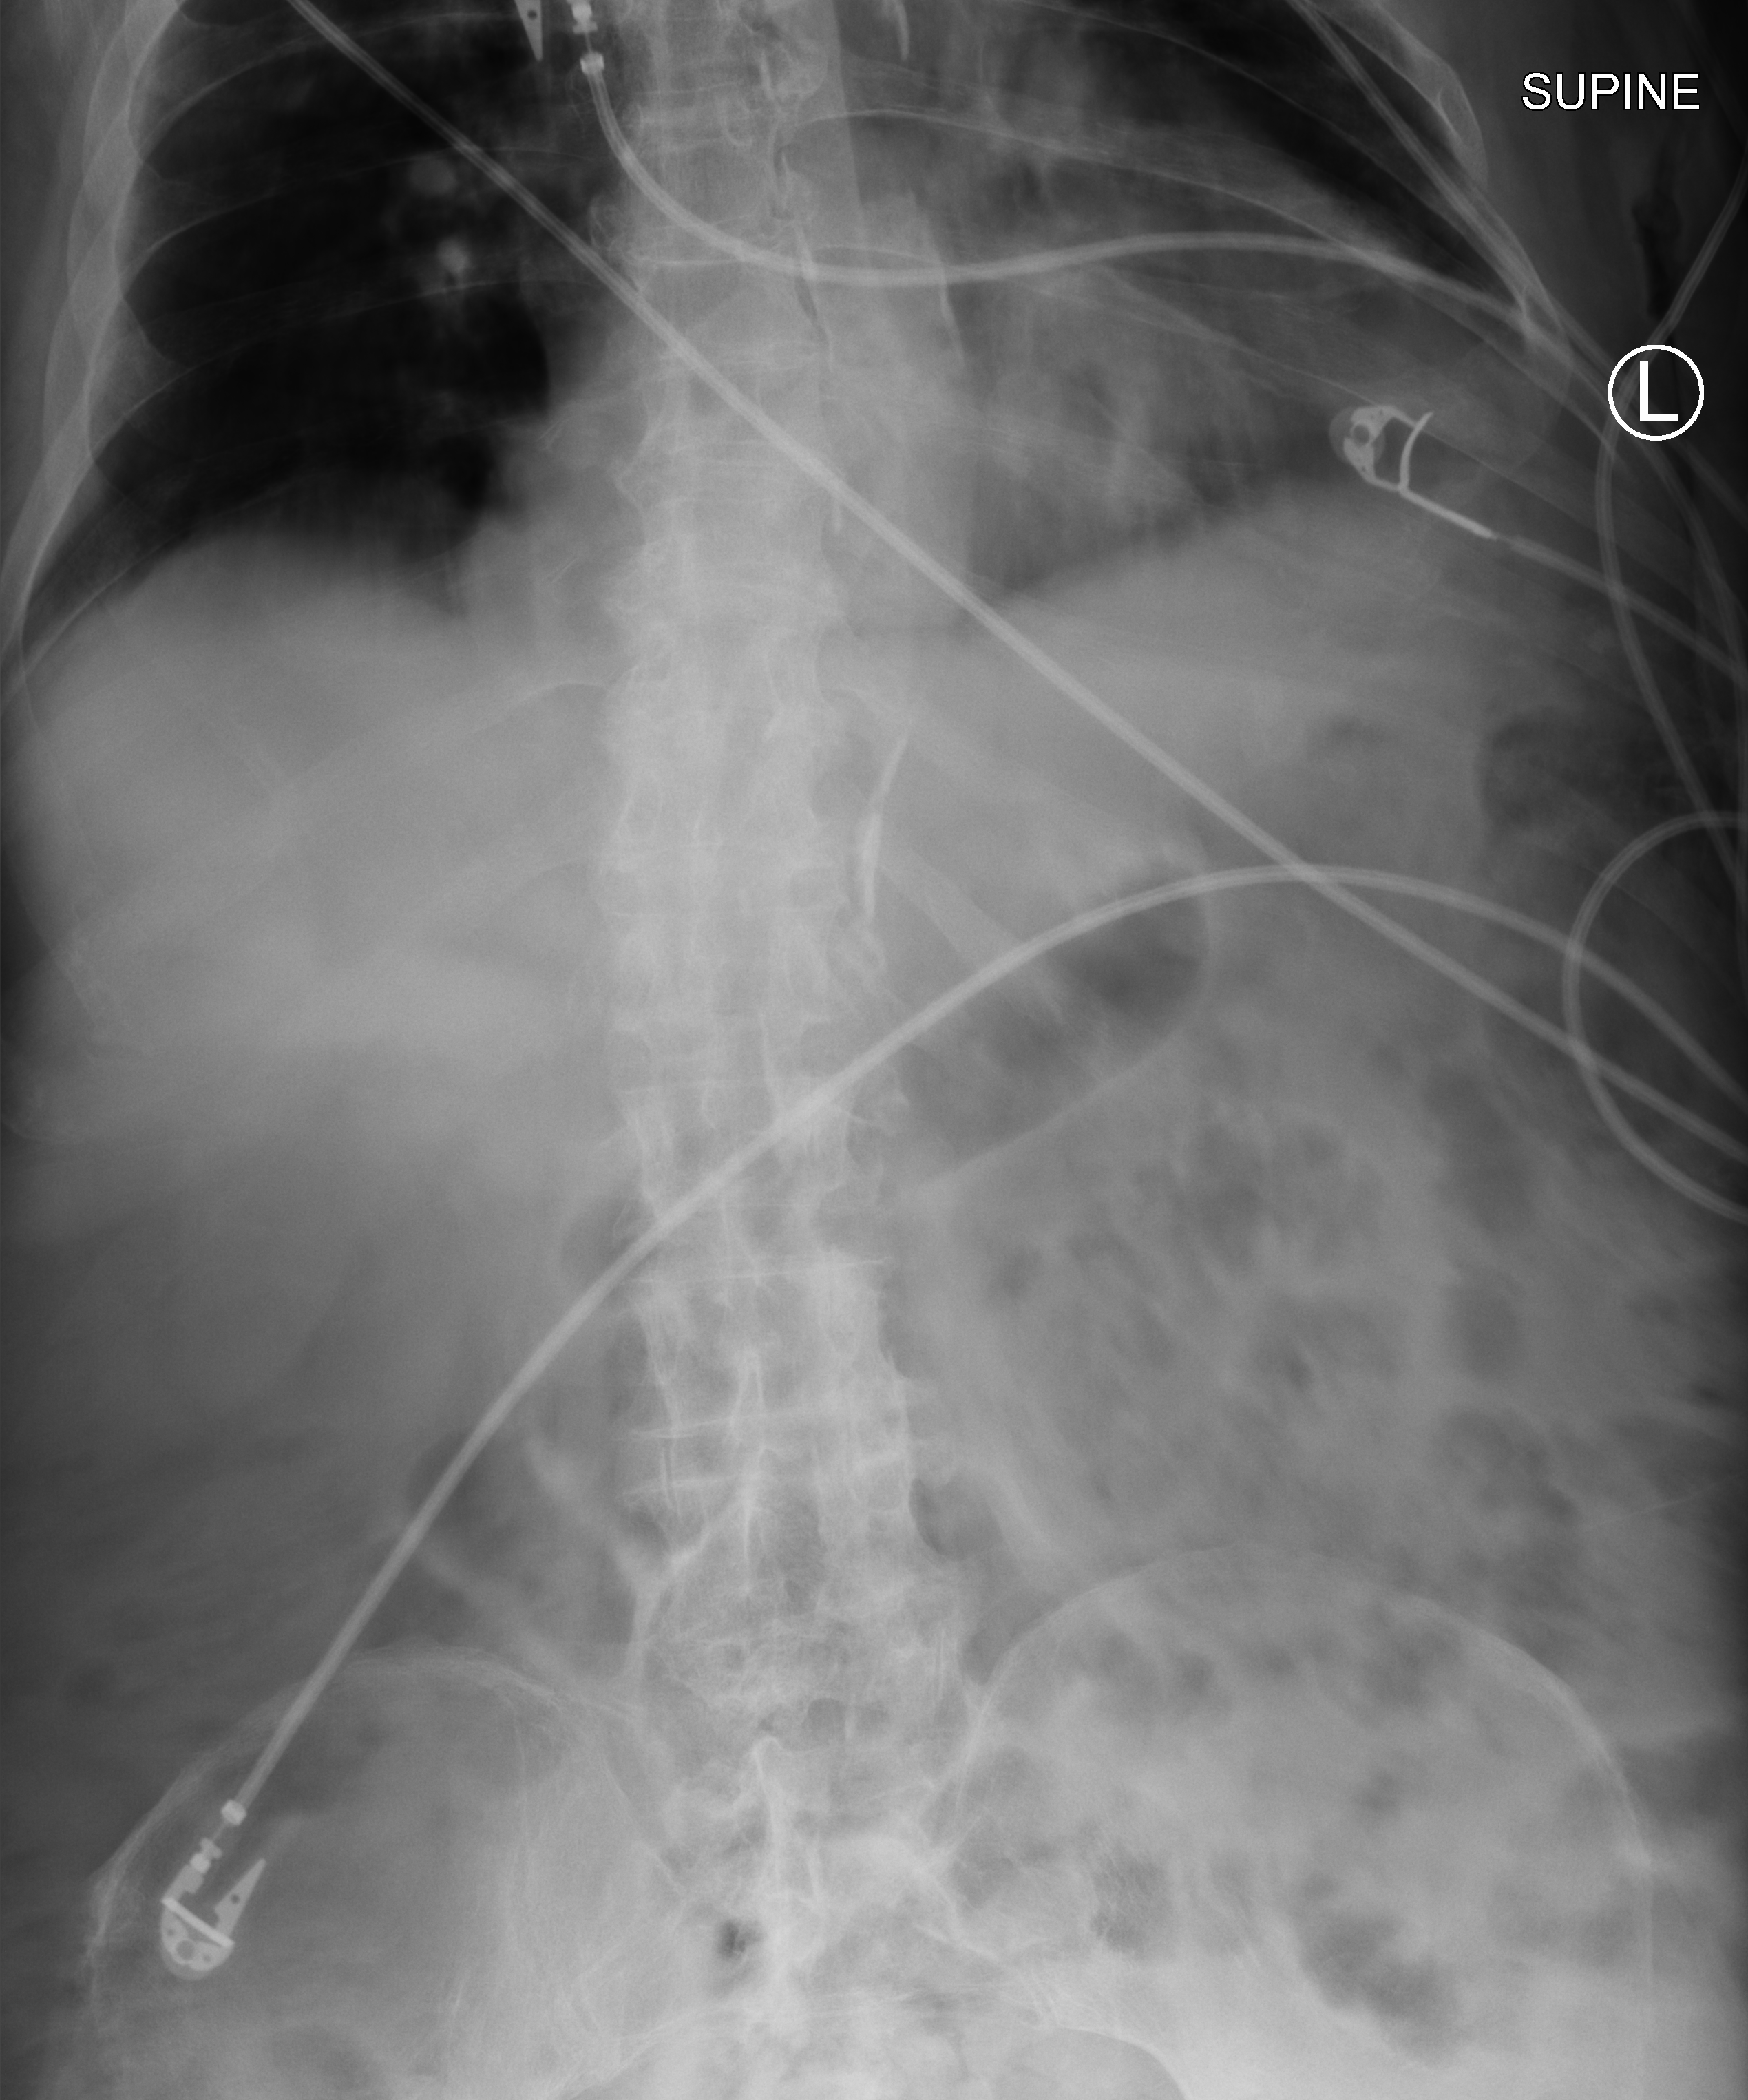
Abdomen X-ray (portable). Patient hospitalised with COVID-19; male, aged 75–90 years.
From the hospital-stay record, not from the radiograph (when in the stay this image was taken is not recorded): other chronic lung disease (admission record): no.